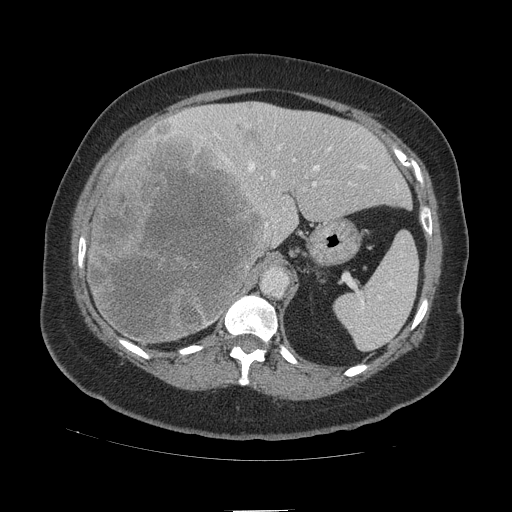
Contrast-enhanced abdominal CT (liver protocol), one axial slice; position 72 of 109 along the scan axis; 140 kVp; soft-tissue window (W 400 / L 40 HU); 2.5 mm slice thickness; 512 × 512 image matrix, field of view 420 × 420 mm. Case-level facts recorded for this patient, not image findings: diagnosis: hepatocellular carcinoma (patient treated with transarterial chemoembolisation; whether this scan precedes or follows treatment is not stated here); TNM stage (as recorded): Stage-IVB; Child-Pugh class: A.
Outlined on this slice (semi-automatic segmentation, software-assisted and operator-edited):
- liver parenchyma outside the tumour (the mass and vessels are separate outlines, so this box may not span the whole liver): bounding box (x1, y1, x2, y2) in pixels: (88, 102, 410, 340)
- mass: (89, 121, 271, 348)
- liver vessels: (174, 118, 397, 187)